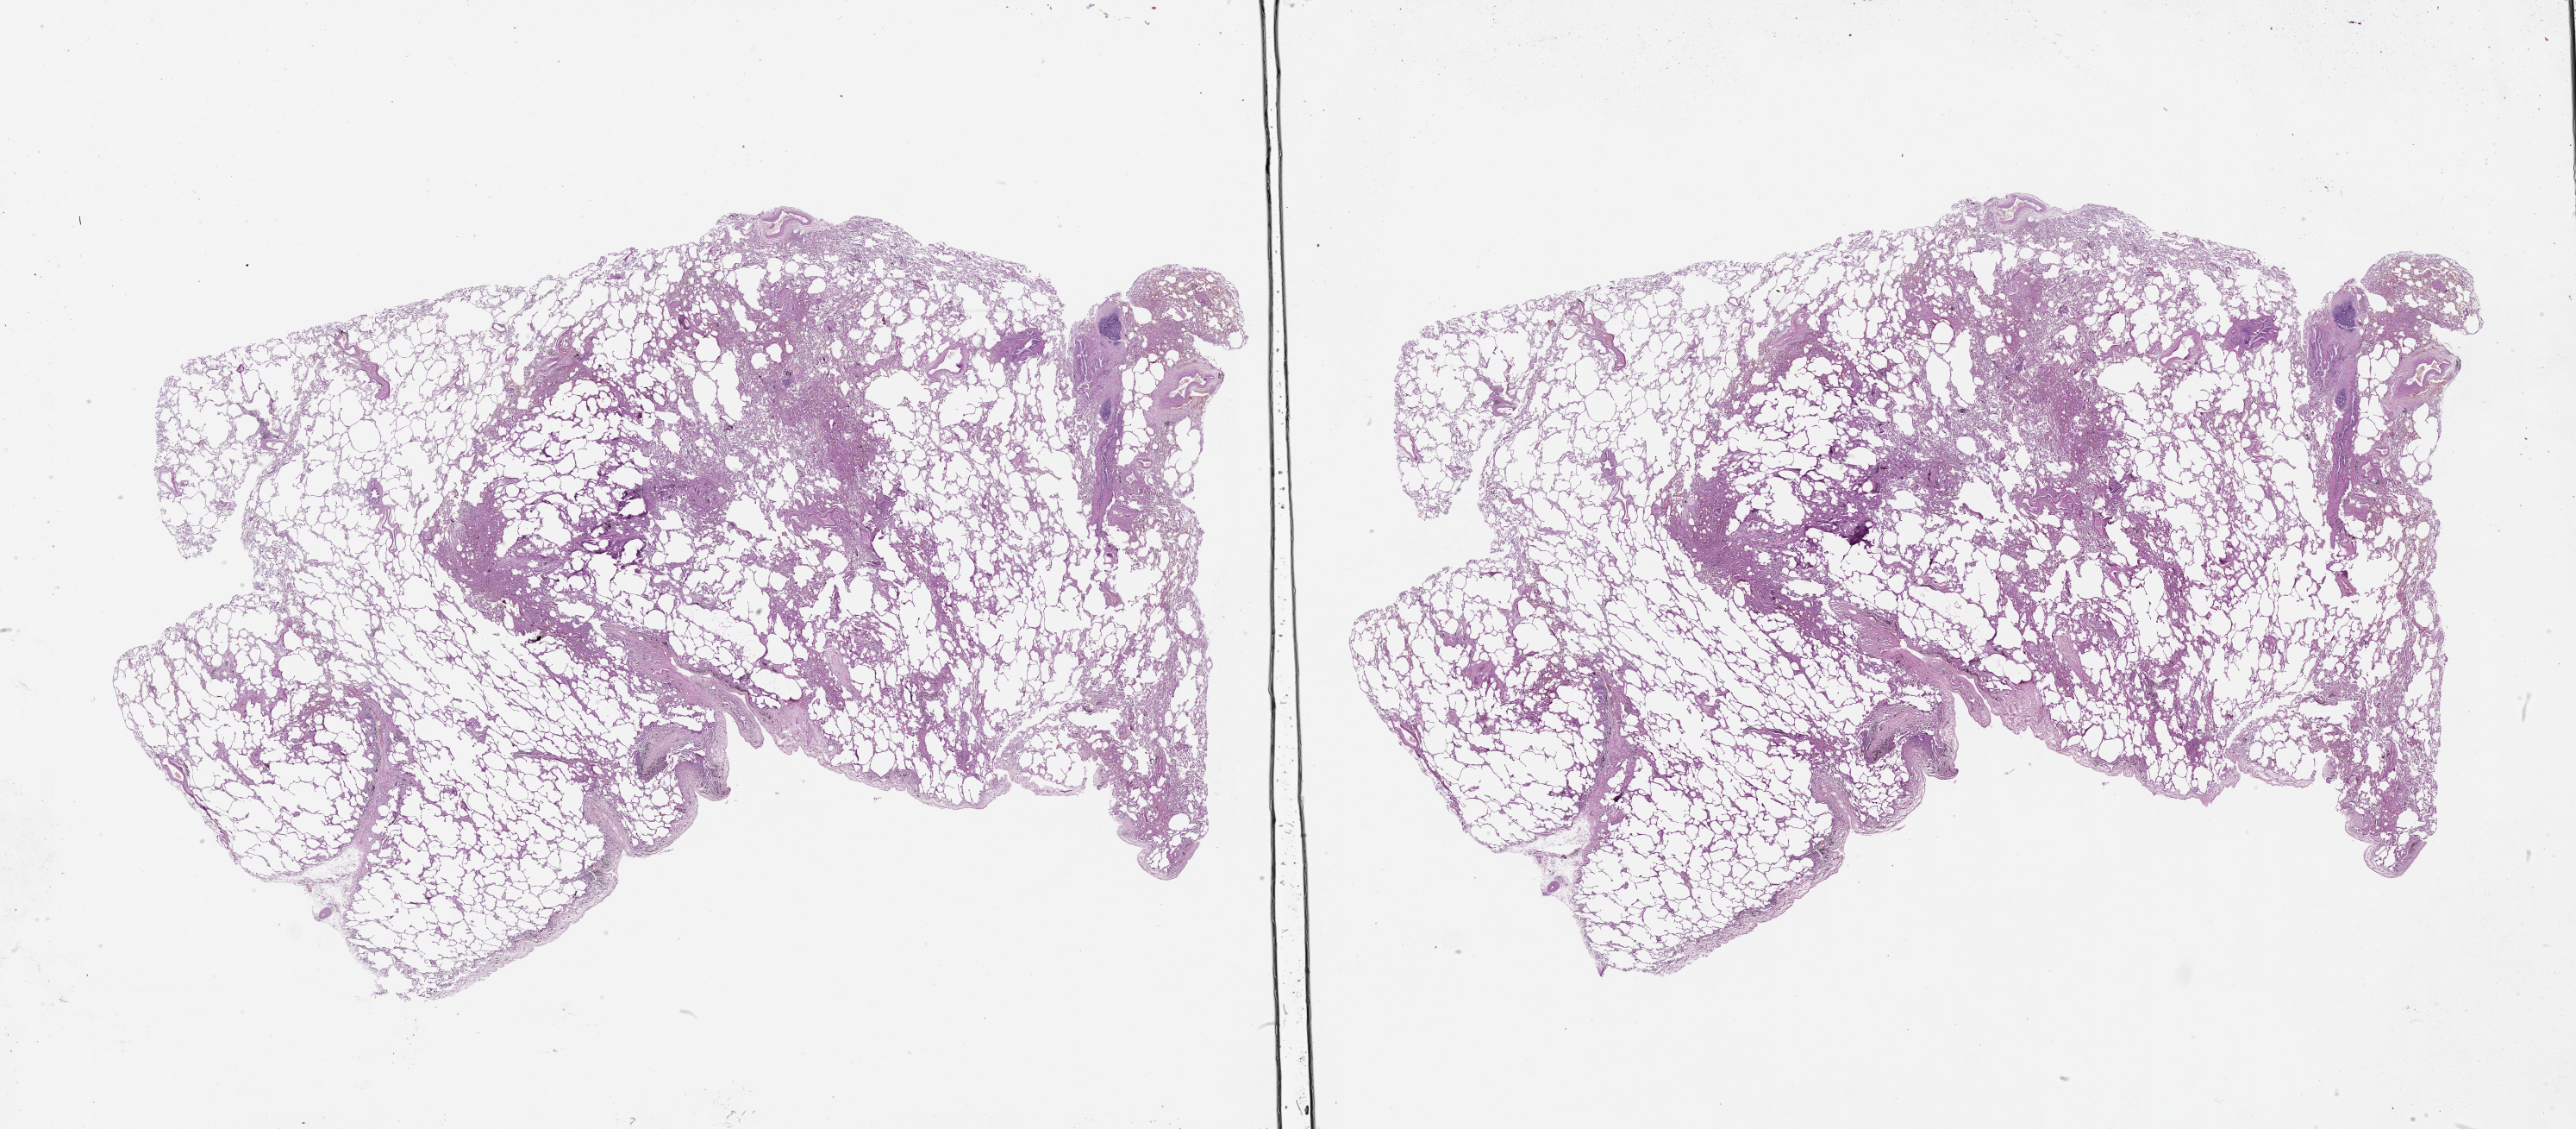
Whole-slide histology image, Hematoxylin and eosin (H&E) stained — low-resolution overview of the scanned area, about 48.1 x 21.1 mm (acquisition: 20x scan). Normal (non-tumour) tissue sample, lung. 65-year-old male patient.
This section: normal (non-tumour) tissue from the same patient. Patient diagnosis (cohort enrolment): squamous cell carcinoma (lung).